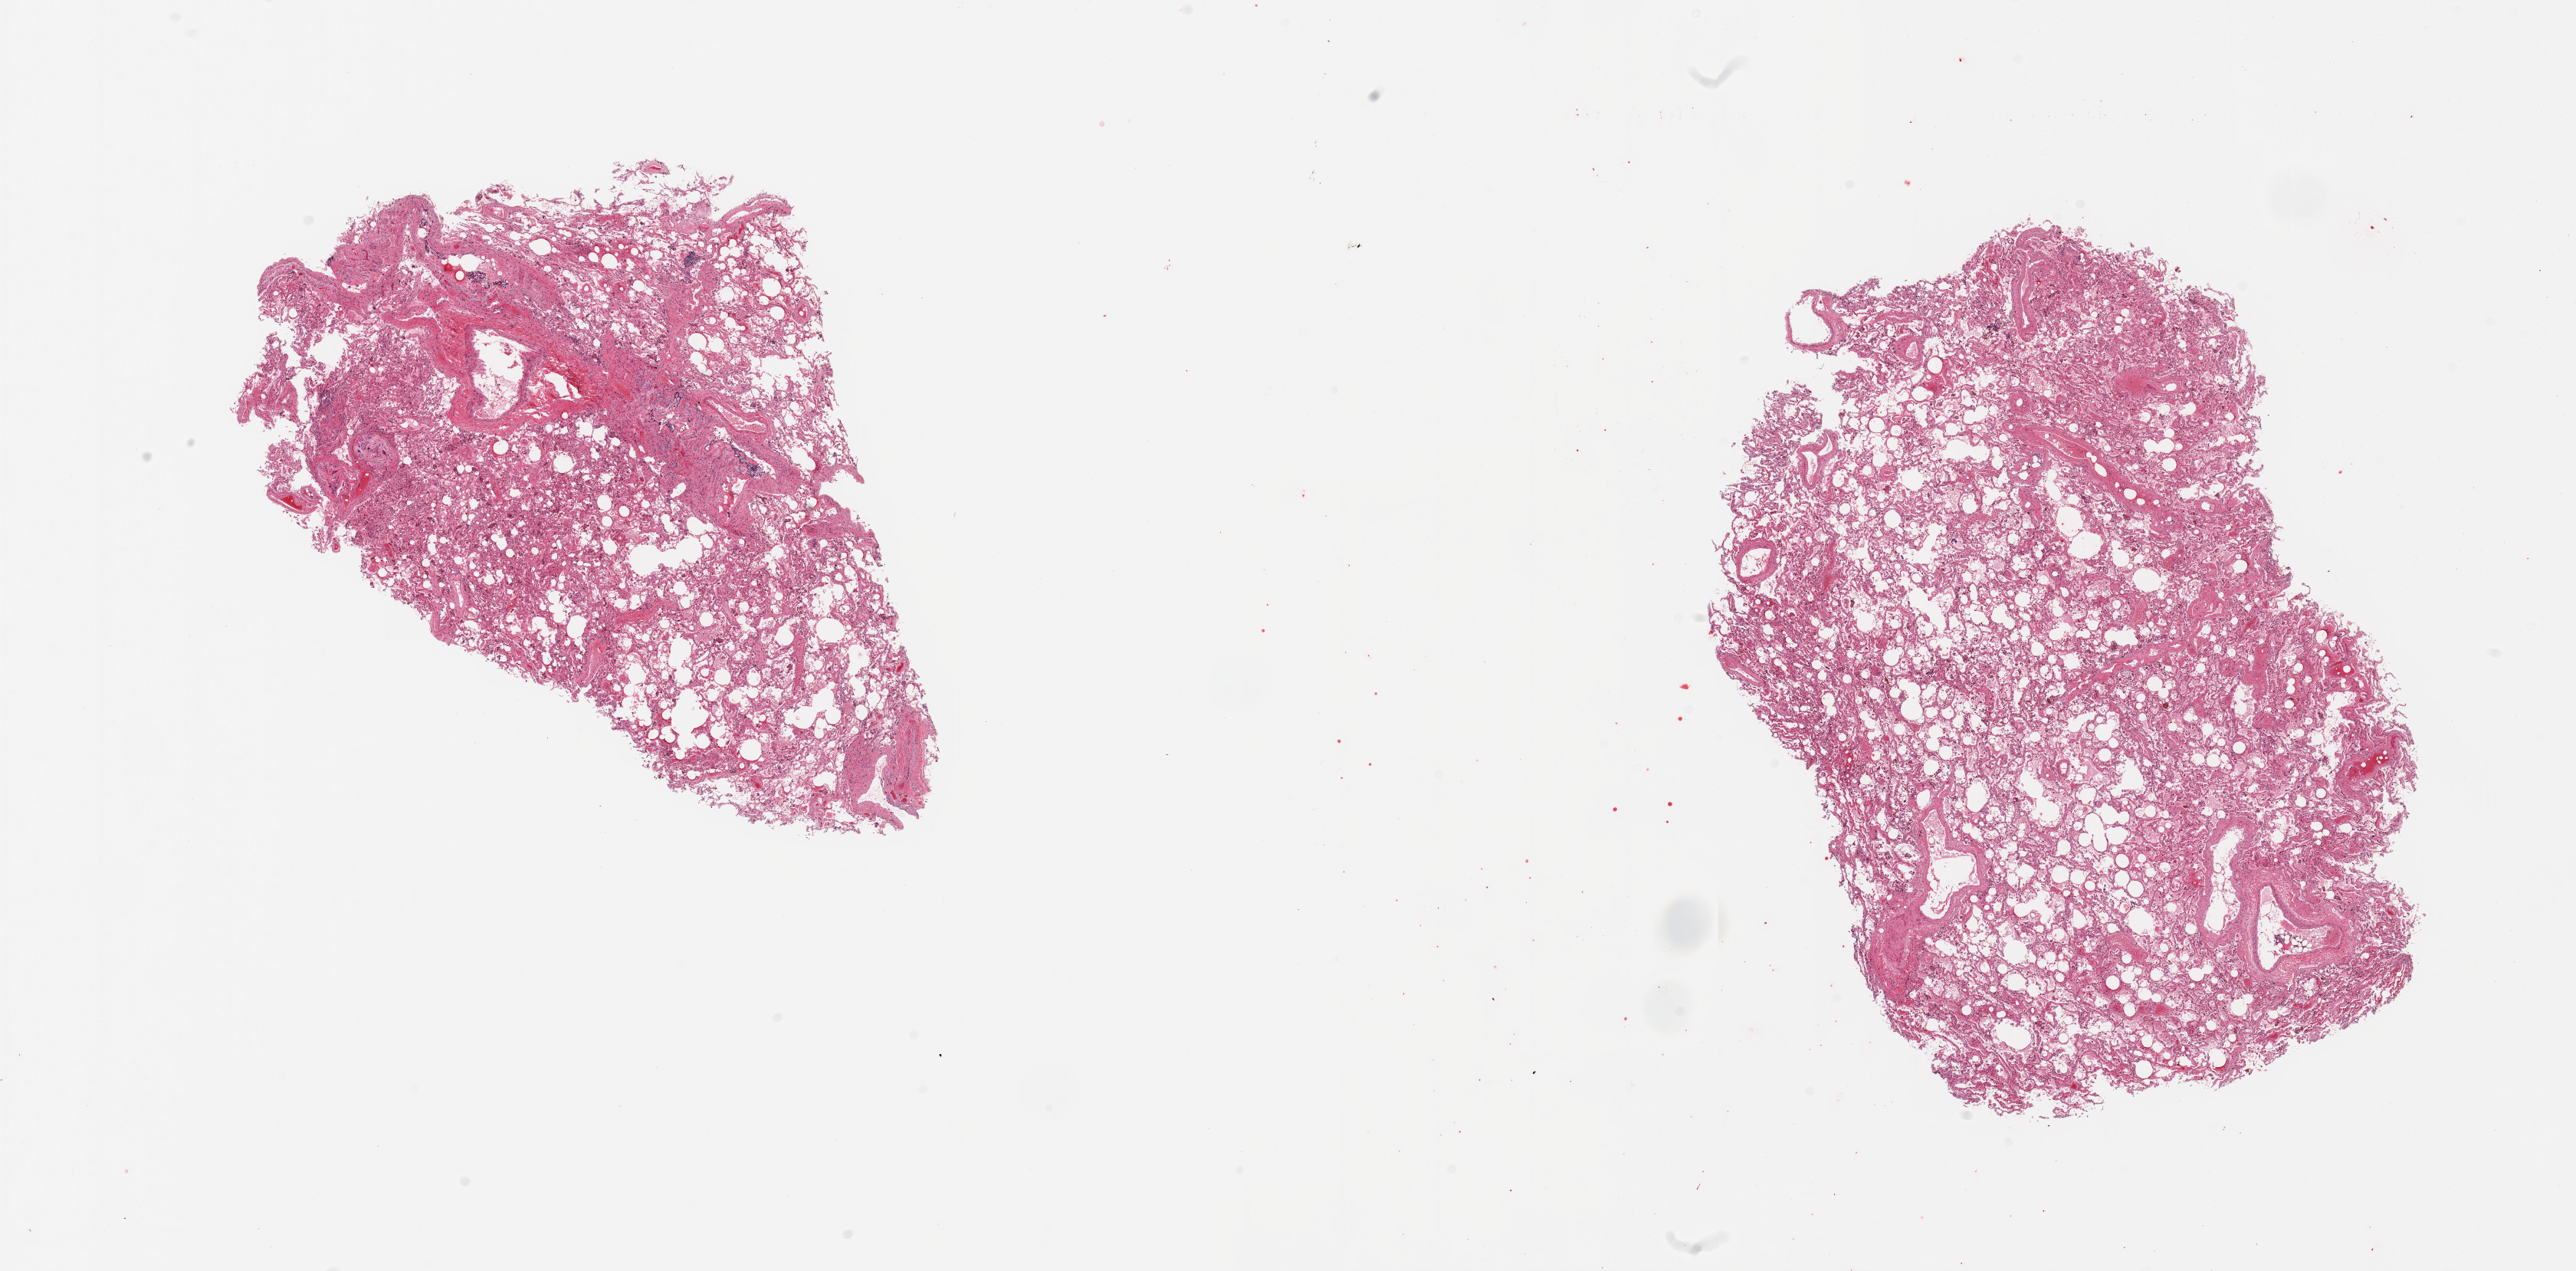
Whole-slide image, hematoxylin and eosin (H&E) stain, shown as a low-resolution overview of the whole scanned area (about 26.6 x 13.1 mm, slide scanned at 20x), PAXgene-fixed, paraffin-embedded tissue, sampled site (target tissue): lung, tissue donor sample. Donor sex: male.
- reviewer comment on this tissue sample: 2 pieces; numerous alveolar macrophages and foreign body reaction